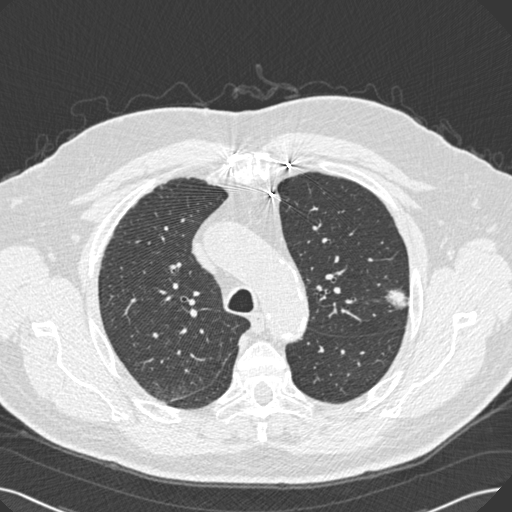
Low-dose screening chest CT, one axial slice. Position 193 of 269 along the scan axis. Reconstruction kernel B30f. 120 kVp. Lung window (W 1500 / L -600 HU). 512 × 512 image matrix, field of view 370 × 370 mm.
Structures marked on this image (expert manual segmentation):
- lesion 1 (tumor, upper lobe of left lung): box from (x=385, y=290) to (x=409, y=312) px